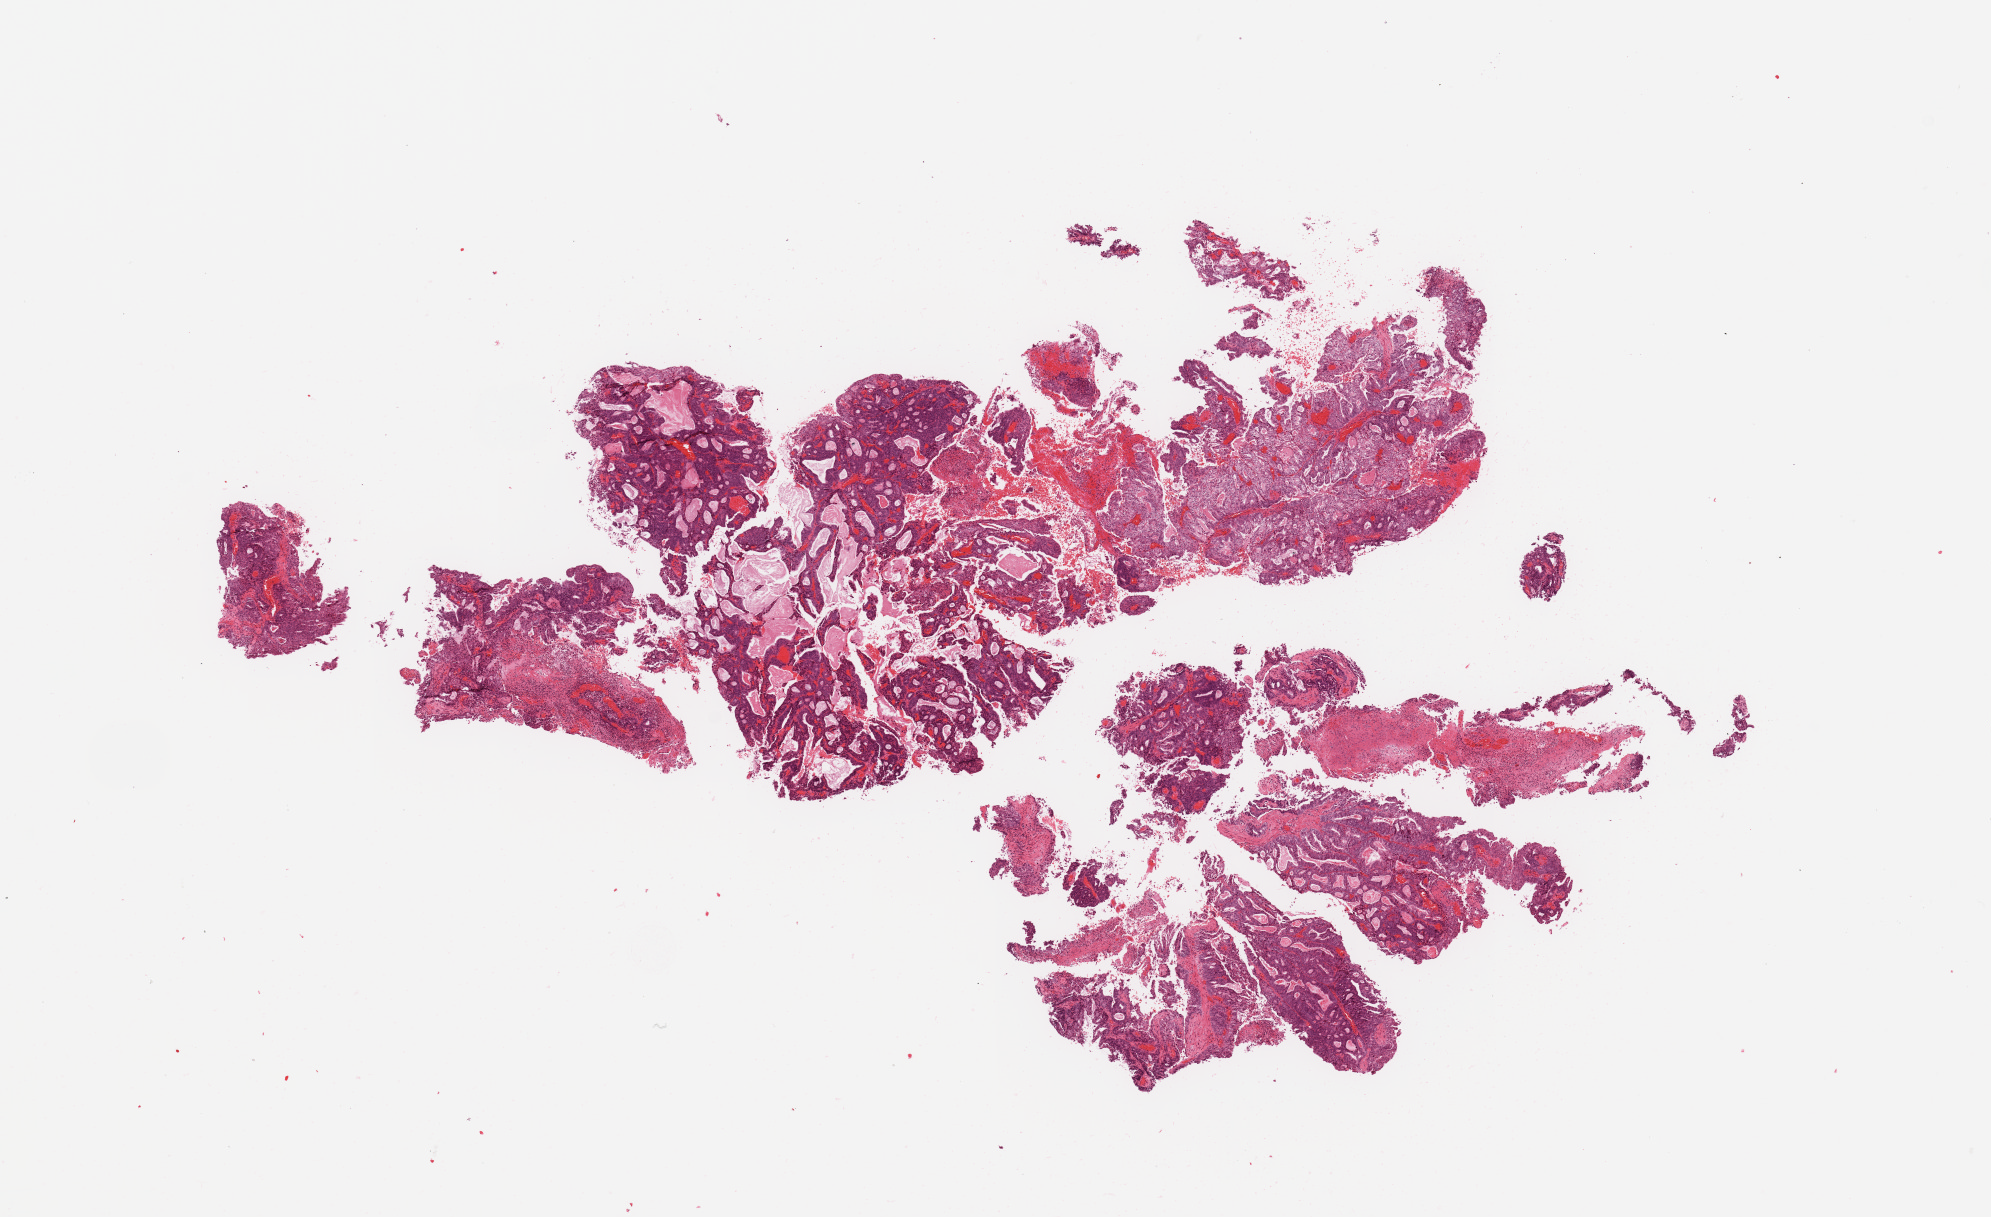
Digitized Hematoxylin and eosin (H&E) stained tissue section (whole slide) — whole scanned area (about 15.8 x 9.6 mm, acquisition: 20x scan) shown as a low-resolution overview, tumour tissue sample, uterus. Patient: female, age 59 years. Histologic grade: G2 (moderately differentiated).
Histologic diagnosis: Endometrioid adenocarcinoma, NOS. AJCC pathologic stage: IA.